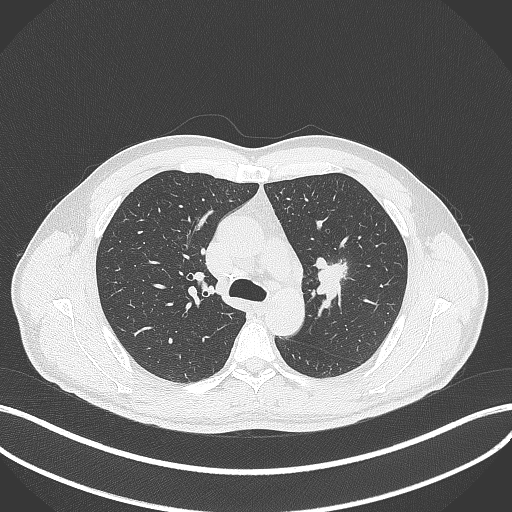
Chest CT, one axial slice. Position 285 of 392 along the scan axis. 120 kVp. Lung window (W 1500 / L -600 HU). 512 × 512 image matrix. Patient: male, 50 years. From the clinical record (not read from this slice): clinical TNM (as recorded): T1c N1 M1b.
Structures marked on this image (rectangle marked by the reading radiologist):
- lung tumour (recorded histology: squamous cell carcinoma): bounding box <313,254,350,295> (left, top, right, bottom; pixels)